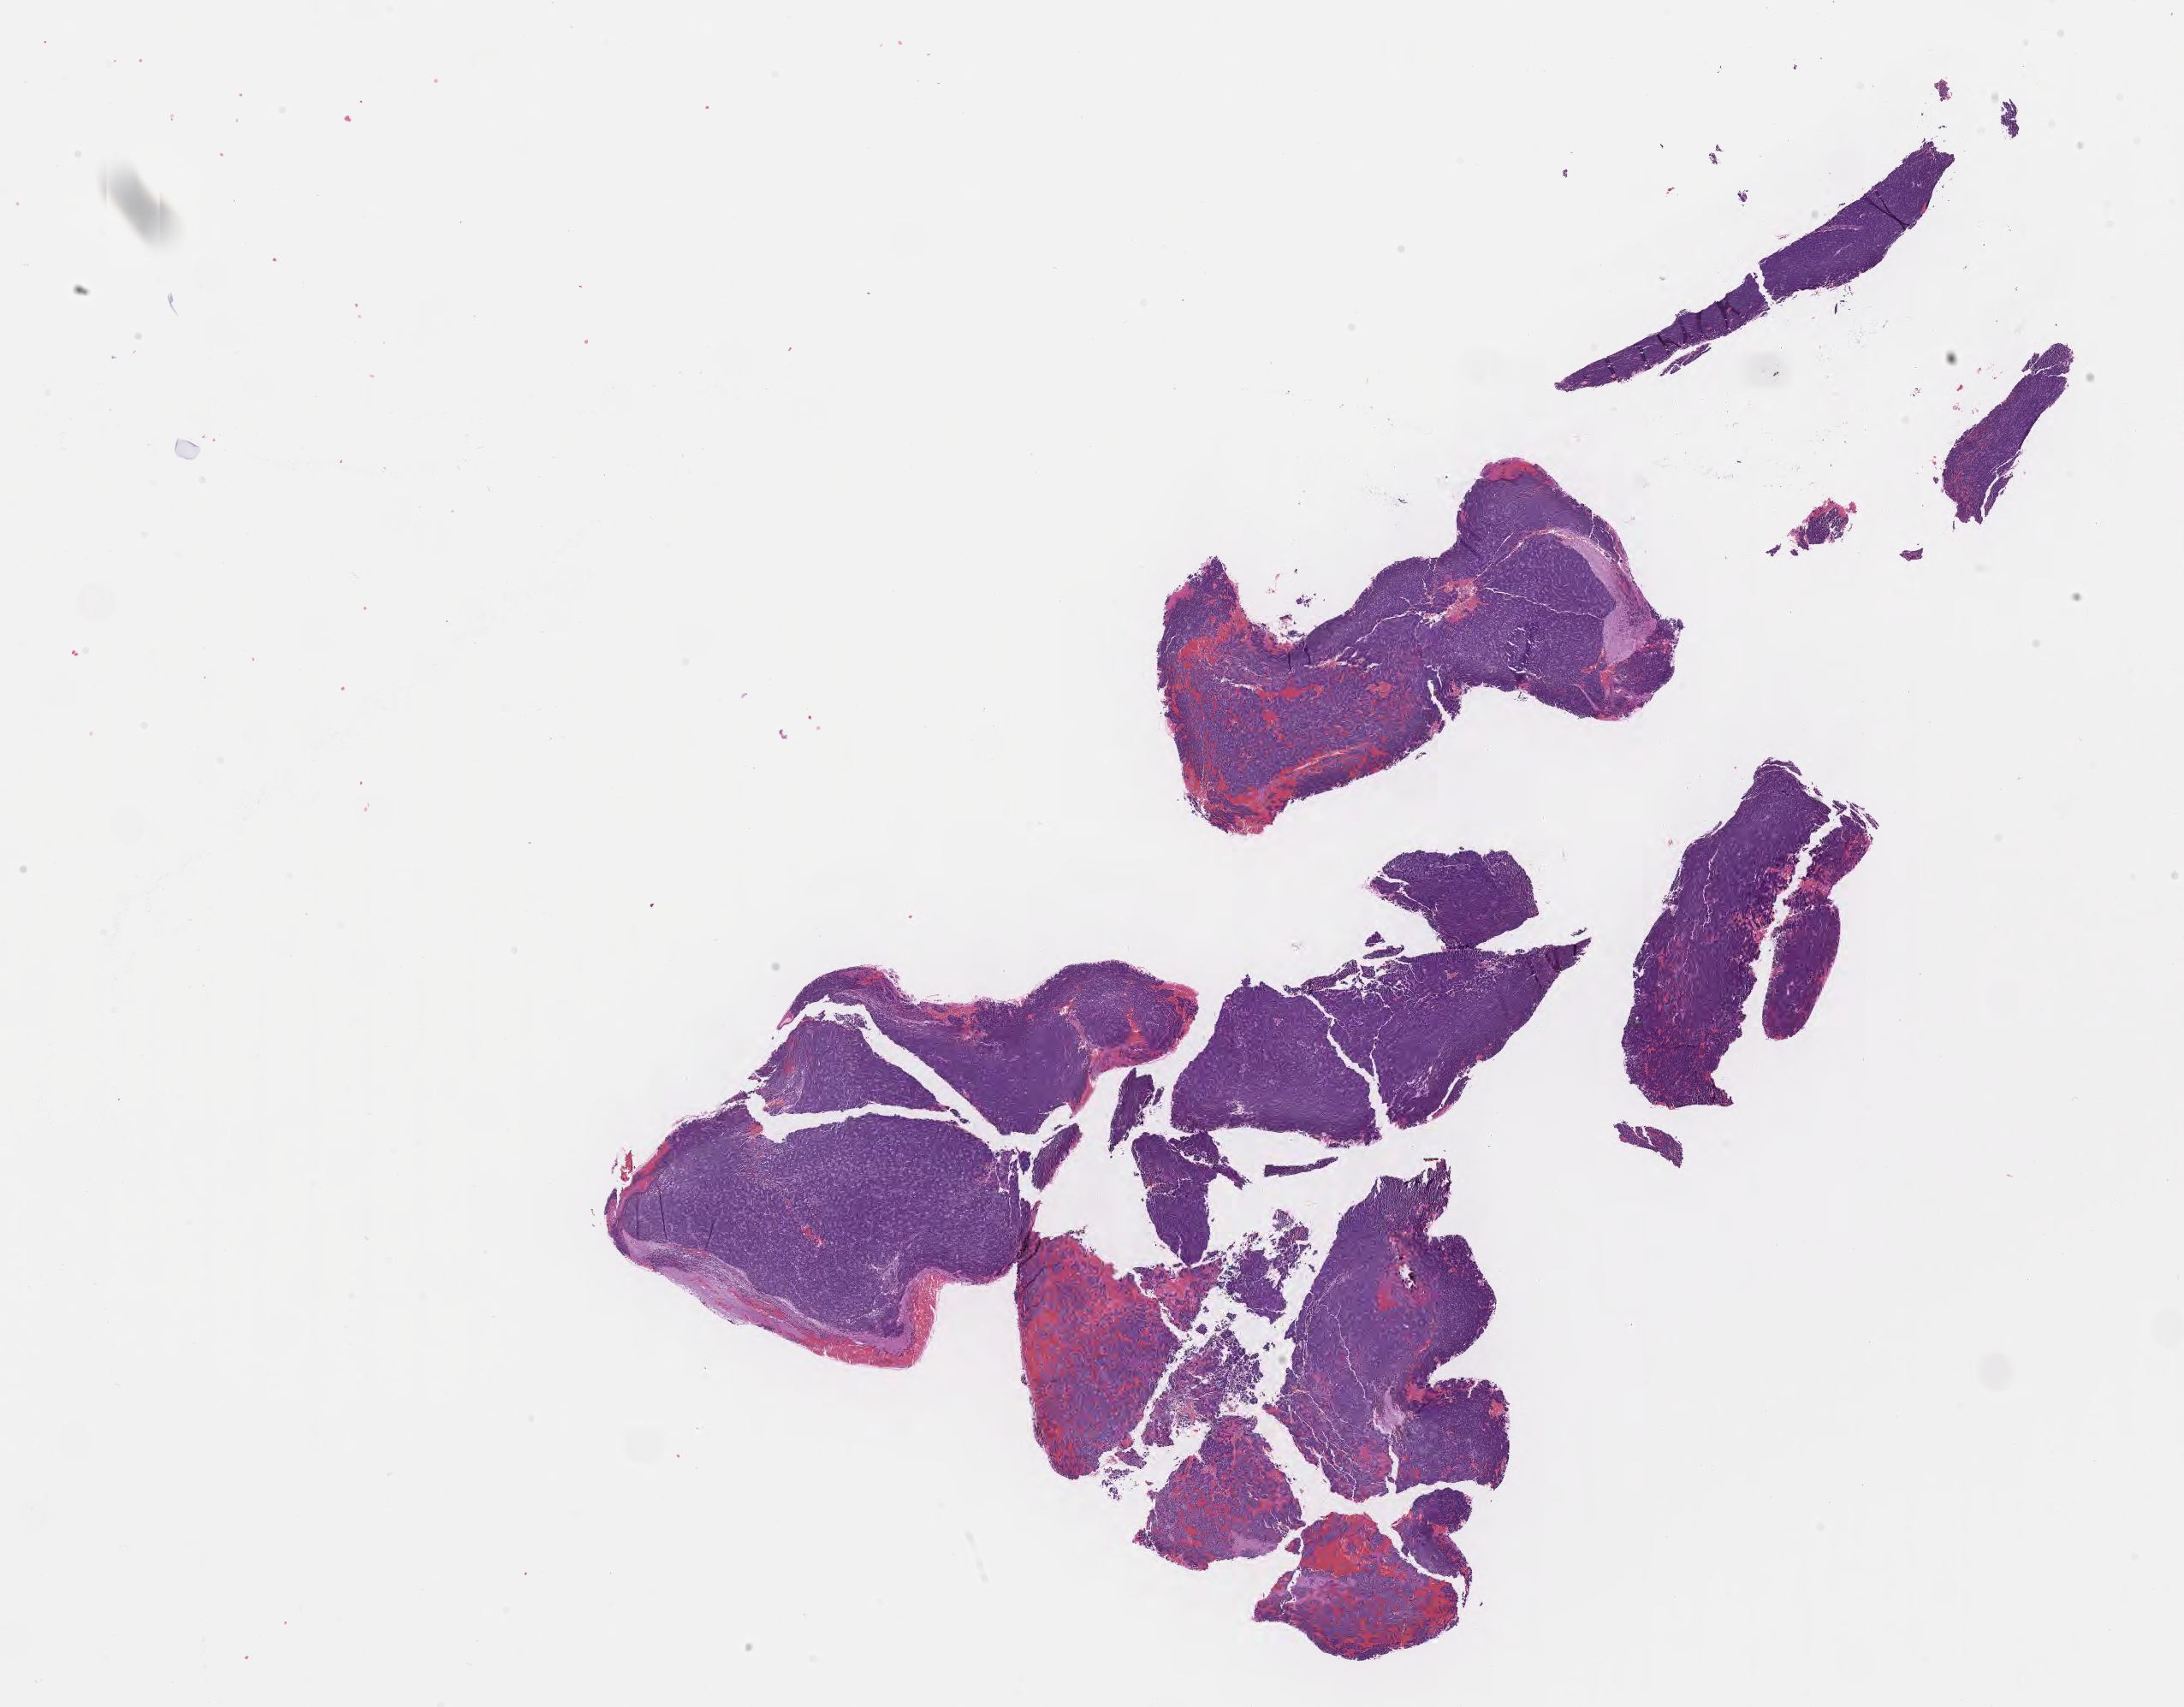
Hematoxylin and eosin (H&E) whole-slide image of tumor tissue from the brain, a low-resolution overview of the entire scanned area, about 20.6 x 16.1 mm; formalin-fixed, paraffin-embedded (FFPE) tissue. Female patient, age 189 months (15 years 9 months).
* diagnosis (ICD-O-3 morphology term): Medulloblastoma, NOS